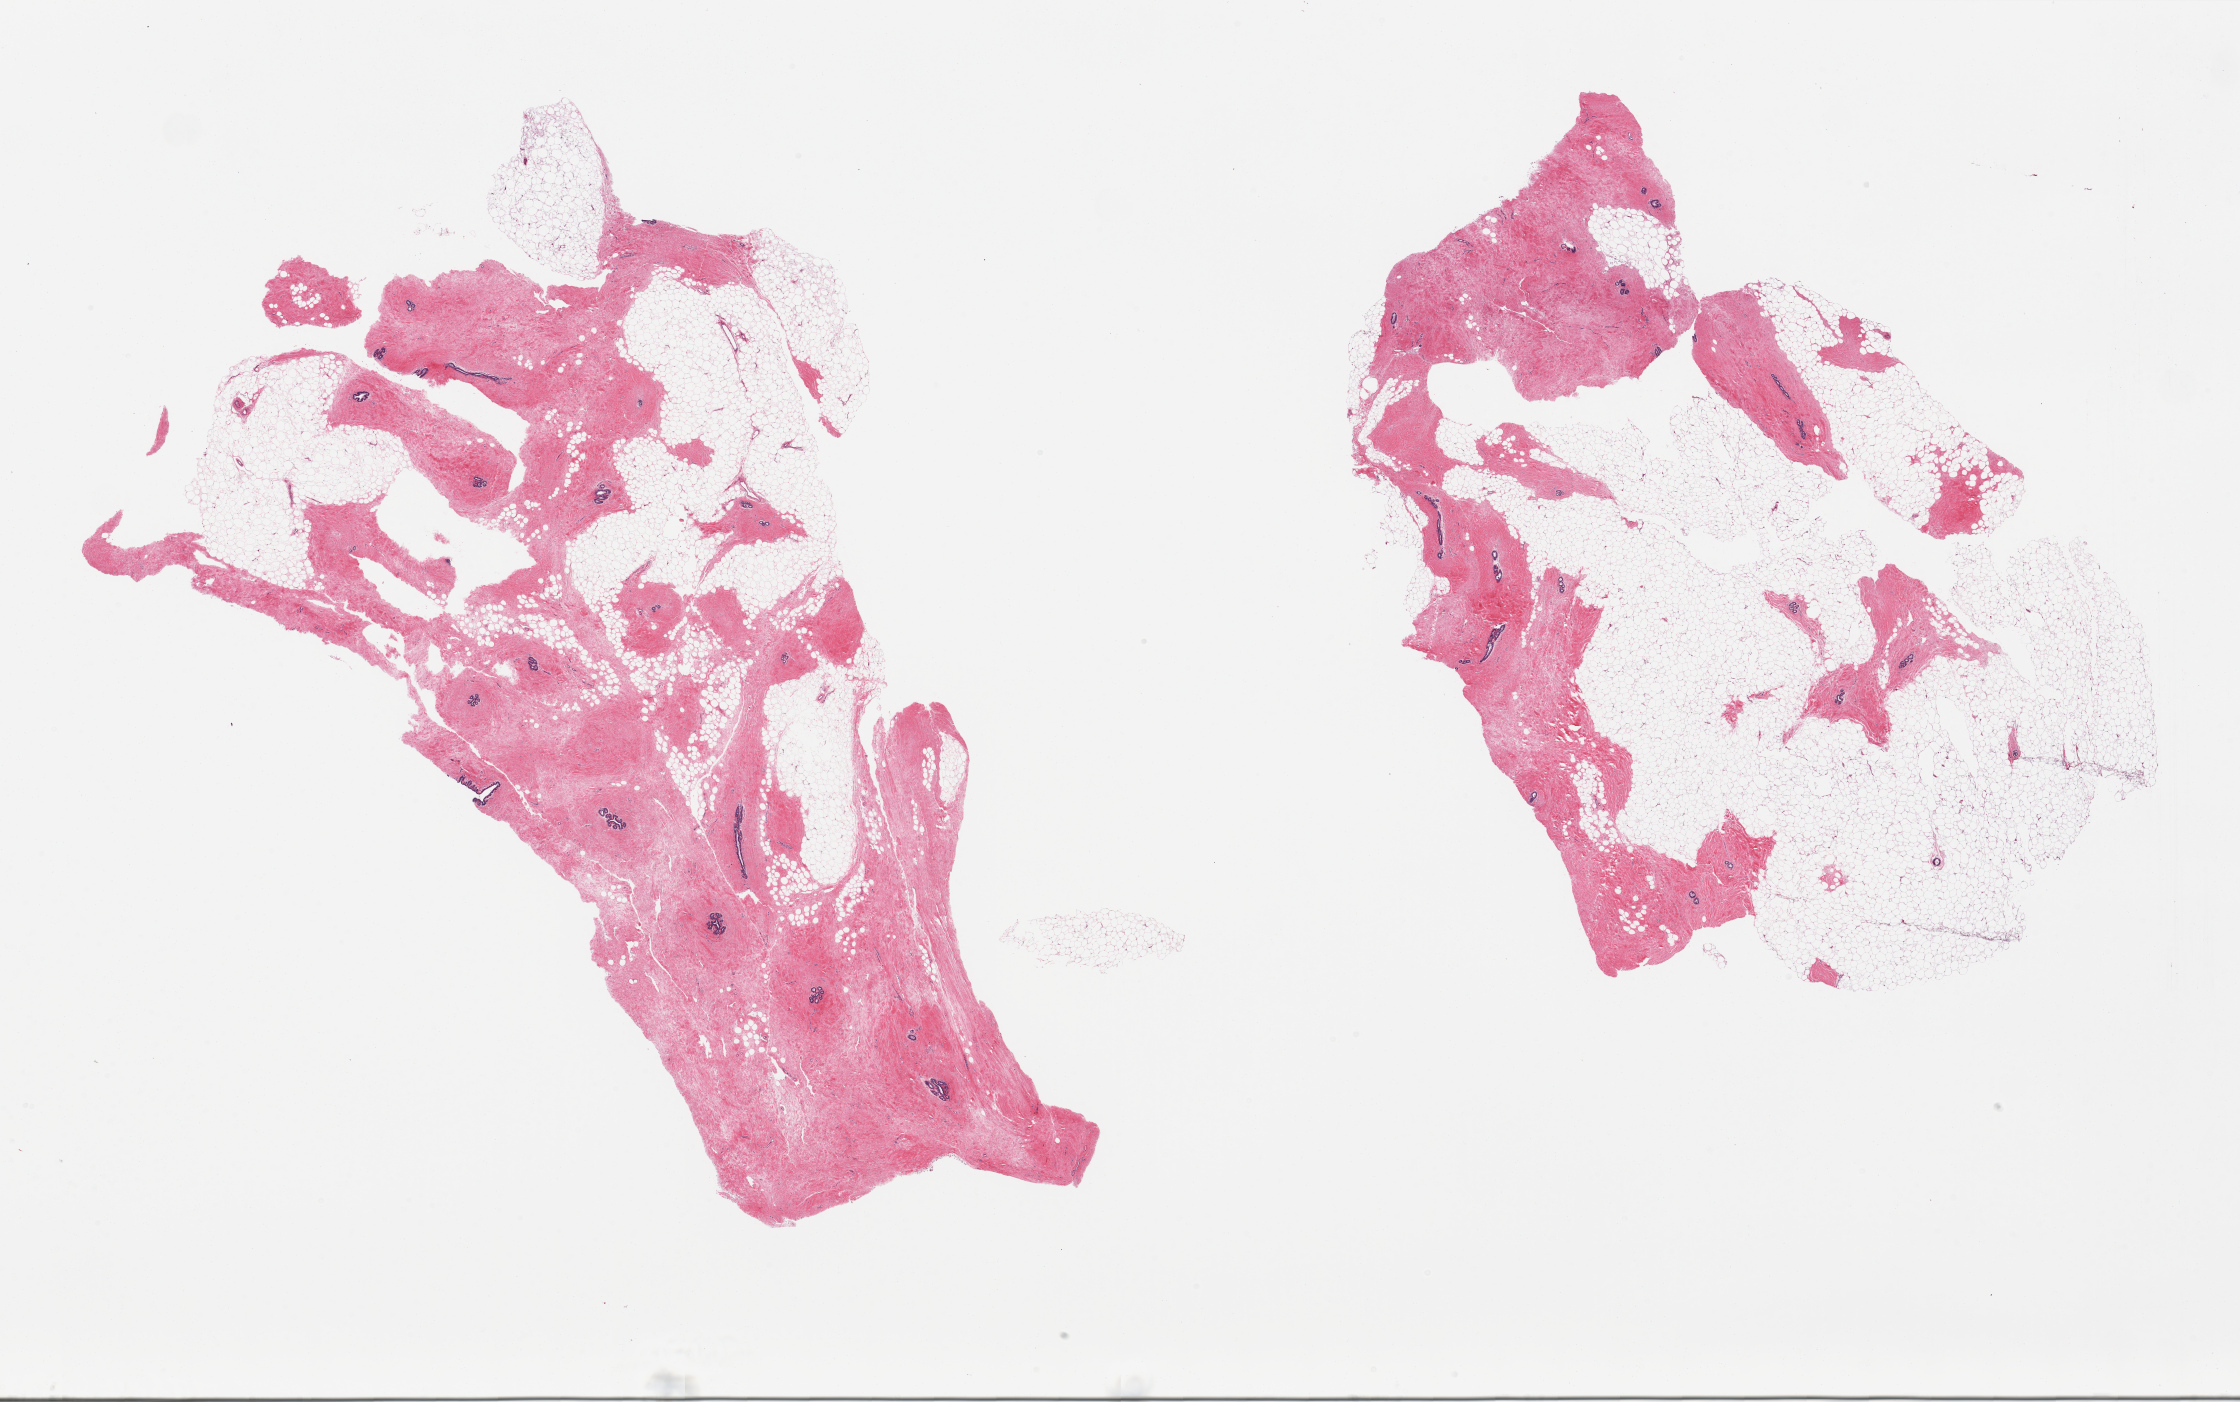
Digitized haematoxylin and eosin-stained section — shown as a low-resolution overview of the whole scanned area (about 35.4 x 22.2 mm, acquisition: 20x scan), PAXgene-fixed, paraffin-embedded tissue, section of breast (target tissue), donor tissue sample. Donor: male.
Pathologist's review note for this sample: 2 pieces, gynecomastoid stromal hyperplasia2.